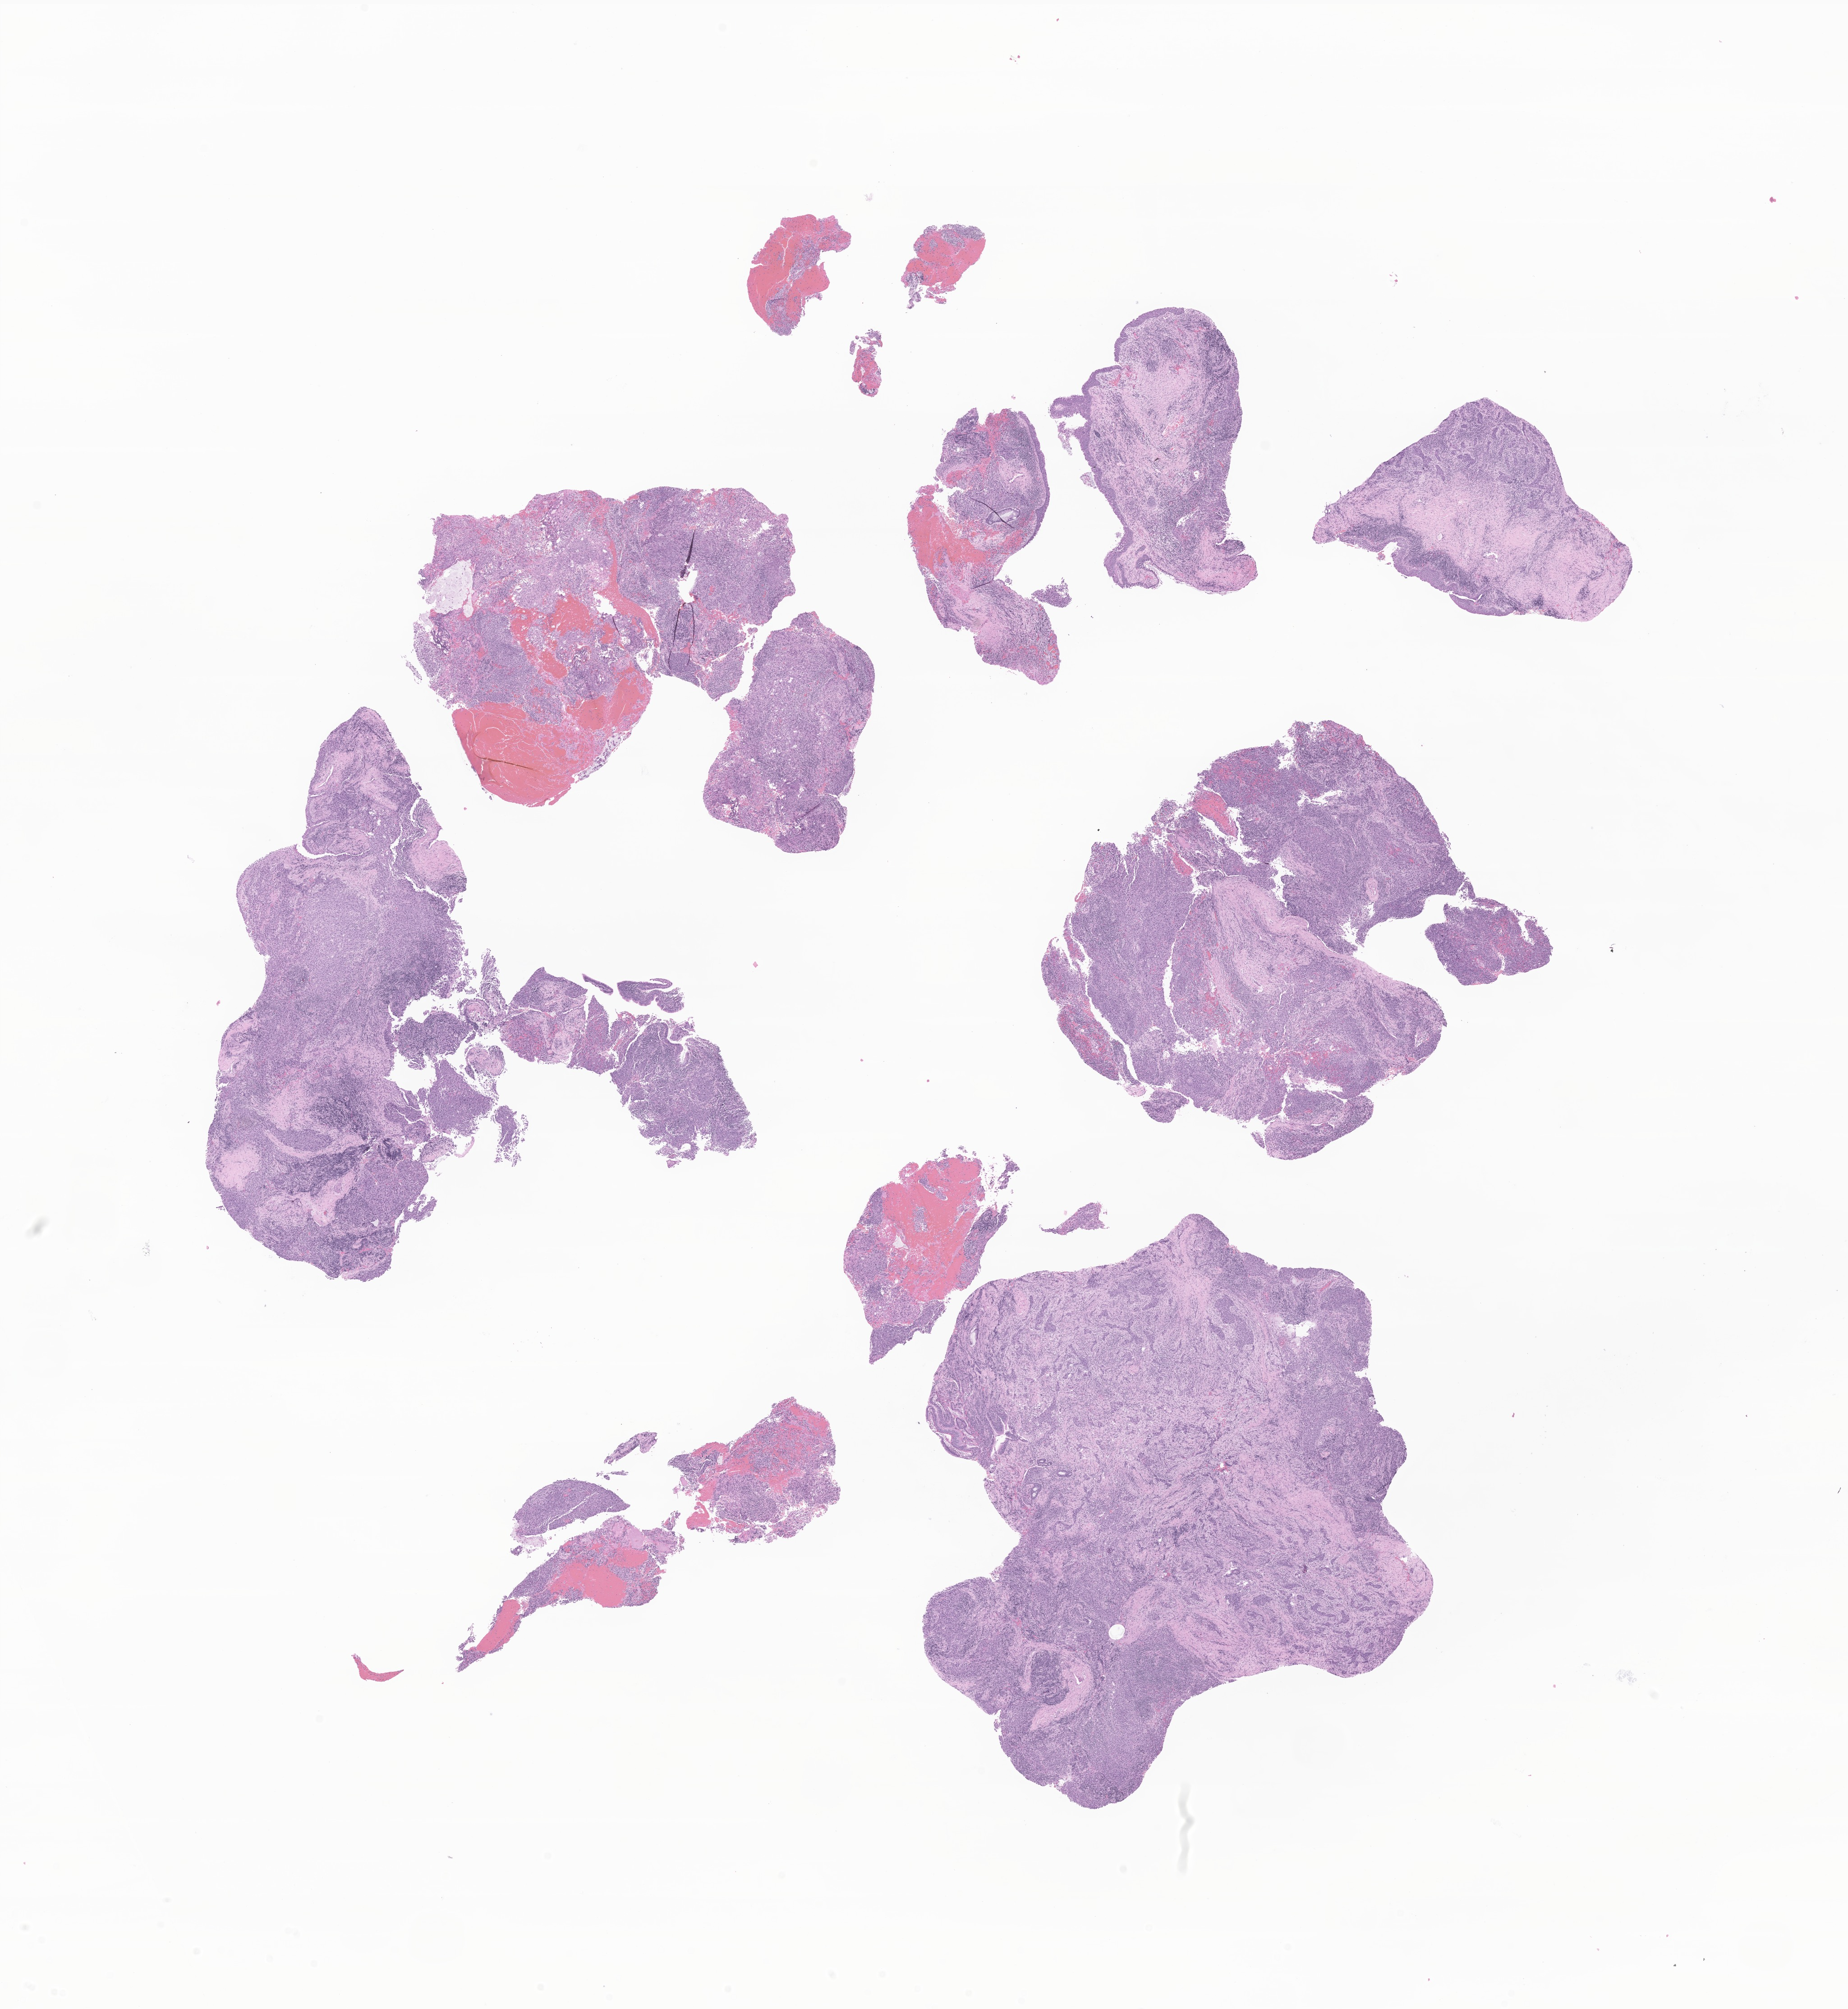
Digitized H&E-stained section of tumor tissue from the nasopharynx — whole scanned area (about 17.3 x 18.8 mm) shown as a low-resolution overview; formalin-fixed paraffin-embedded section. Male patient, age 205 months (17 years 1 month).
Diagnosis: Carcinoma, NOS.